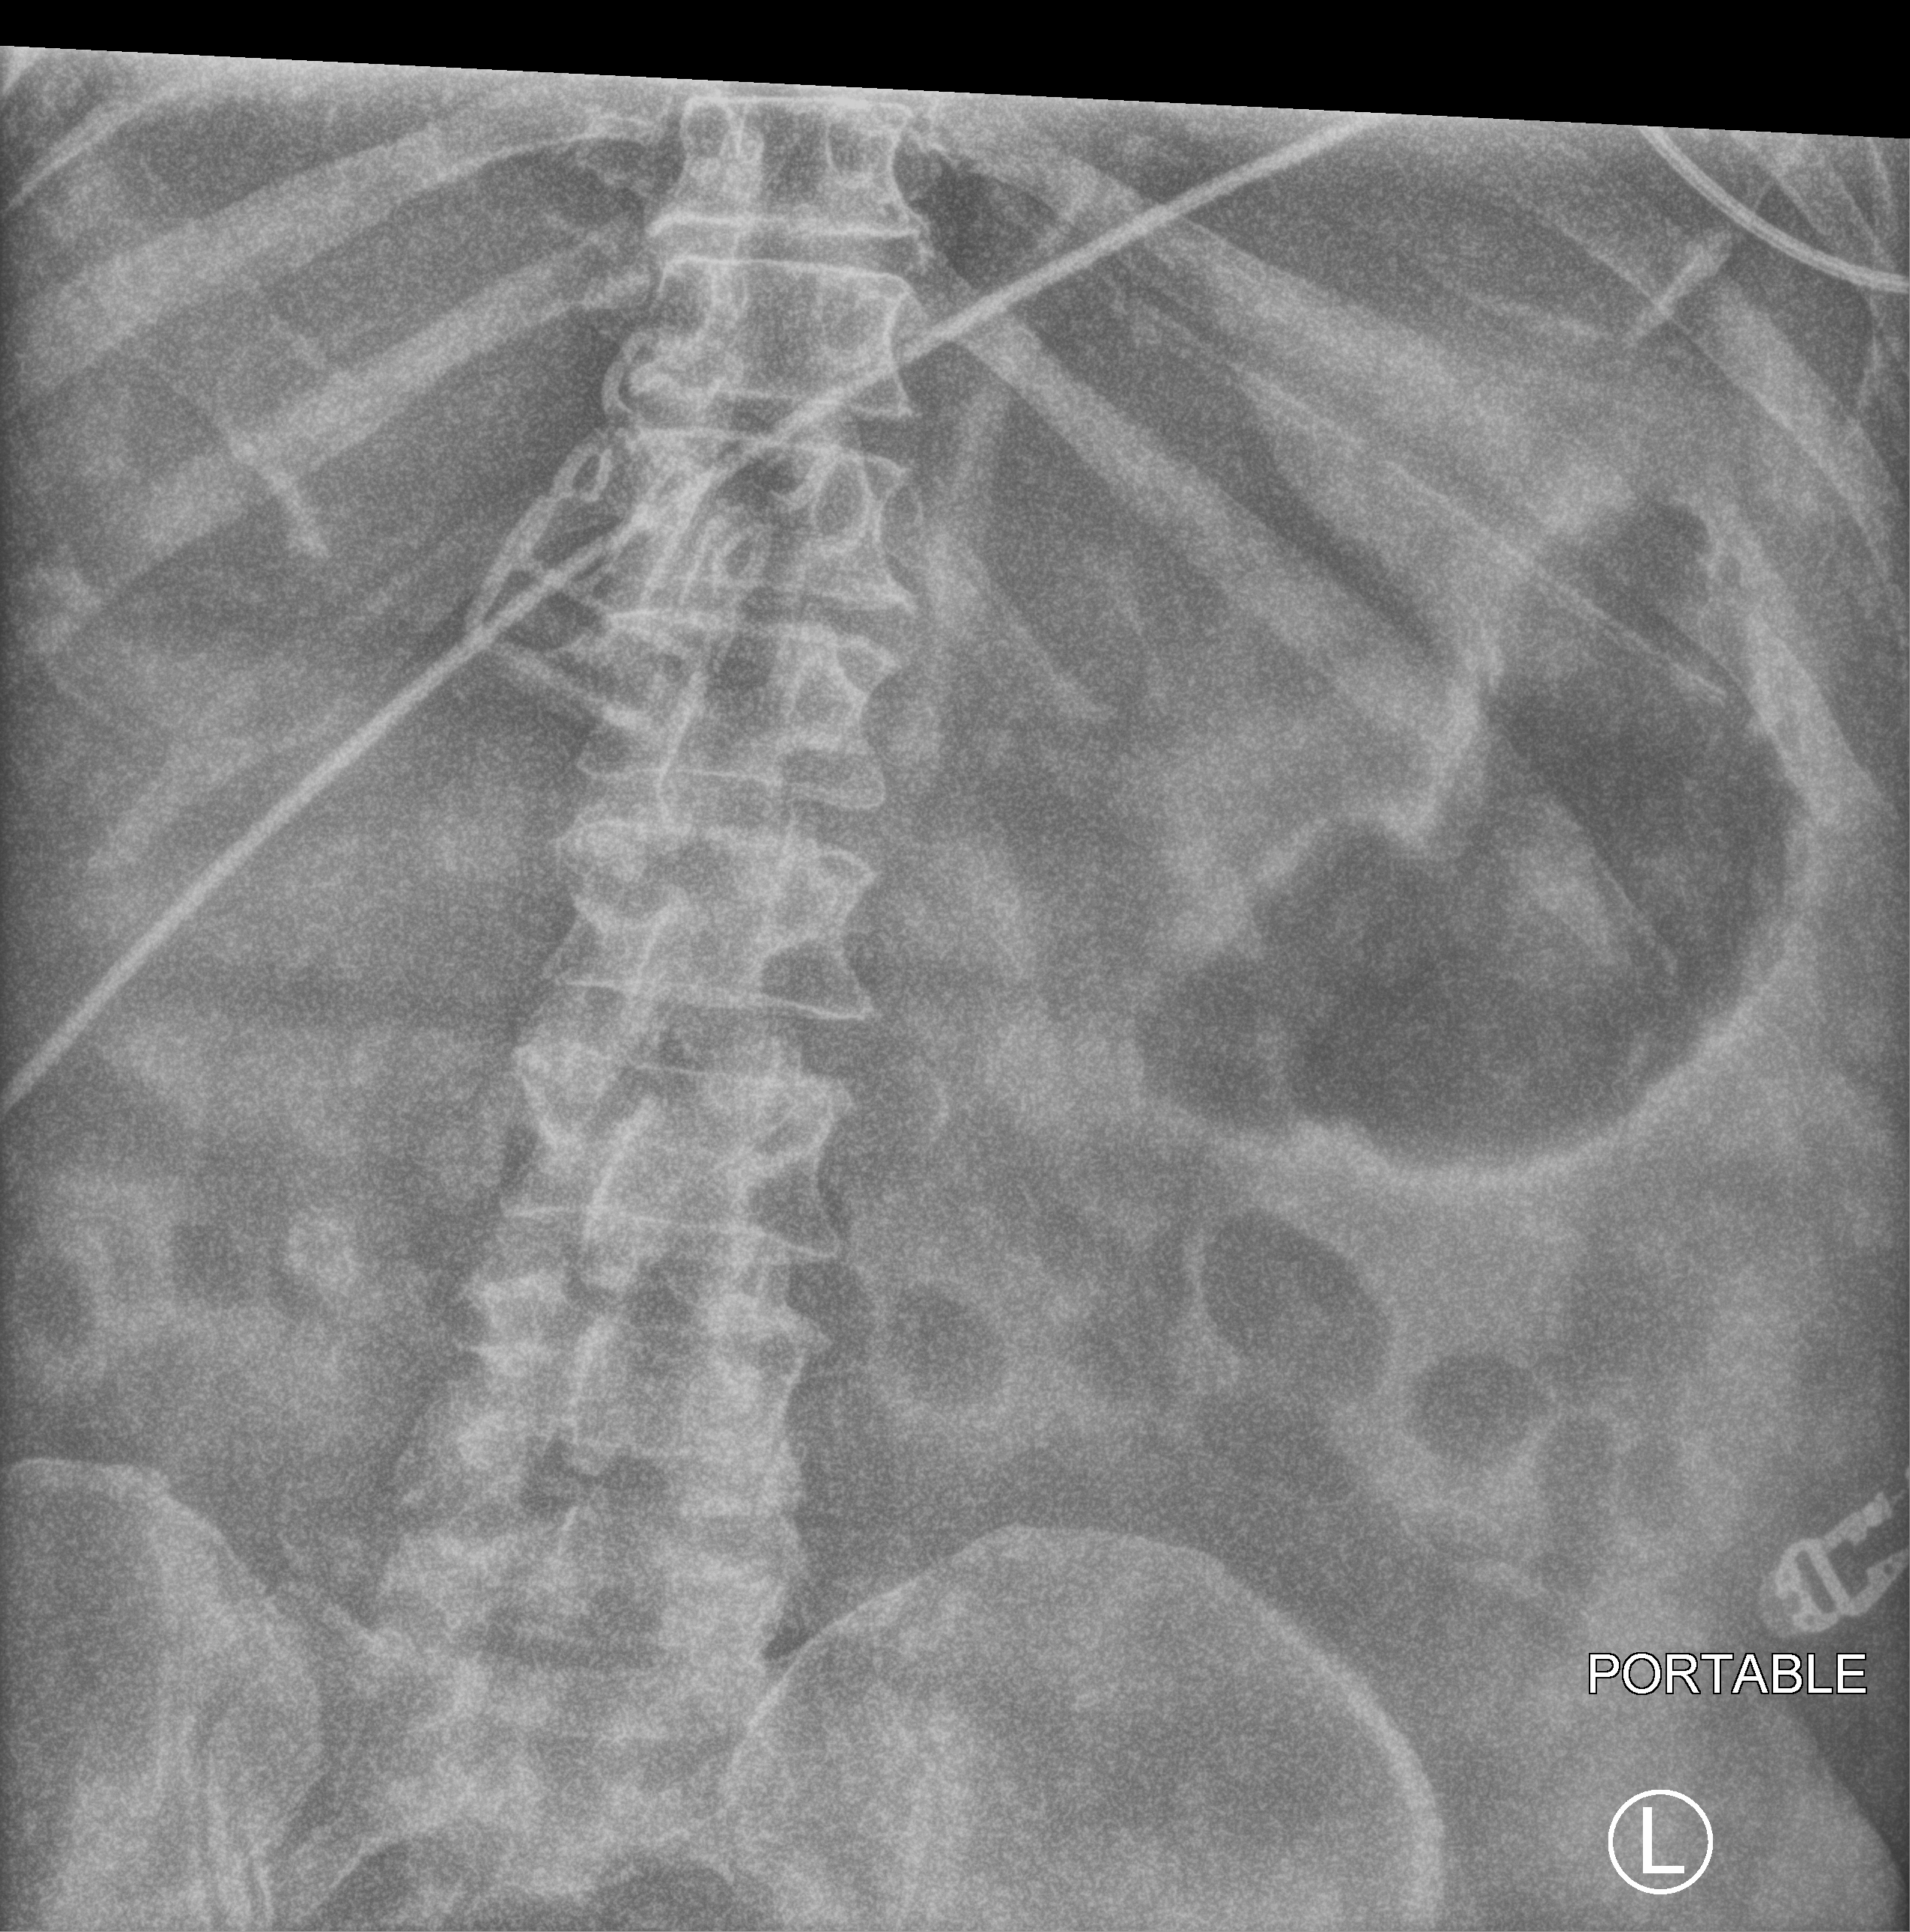
Abdomen X-ray (portable). Patient hospitalised with COVID-19, aged 18–59 years.
Admission-level facts for this patient (not findings on this image; timing relative to this image not recorded):
- mechanically ventilated during this hospital stay: yes
- admitted to intensive care during this hospital stay: yes
- smoking status (admission record): never